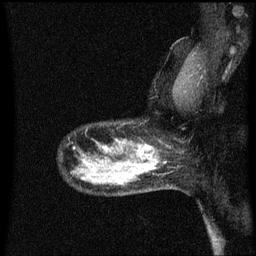
Breast MRI (dynamic contrast-enhanced), one sagittal slice. Position 49 of 60 along the scan axis. Dynamic contrast-enhanced series, image 2 of 3 at this slice position (ordered by acquisition). 1.5 T. TE 4.2 ms, TR 8.4 ms. 2 mm slice thickness. 256 × 256 image matrix. Female patient, age 50 years.
Annotated regions visible in this slice (semi-automatically segmented with operator editing):
- analysis volume of interest (the breast-tissue region the enhancement analysis was run in; not a lesion): bounding box (x1, y1, x2, y2) in pixels: (100, 142, 153, 171)
- tumour enhancement mask (voxels above the 70 % enhancement threshold inside the analysis volume of interest): (137, 144, 153, 171)